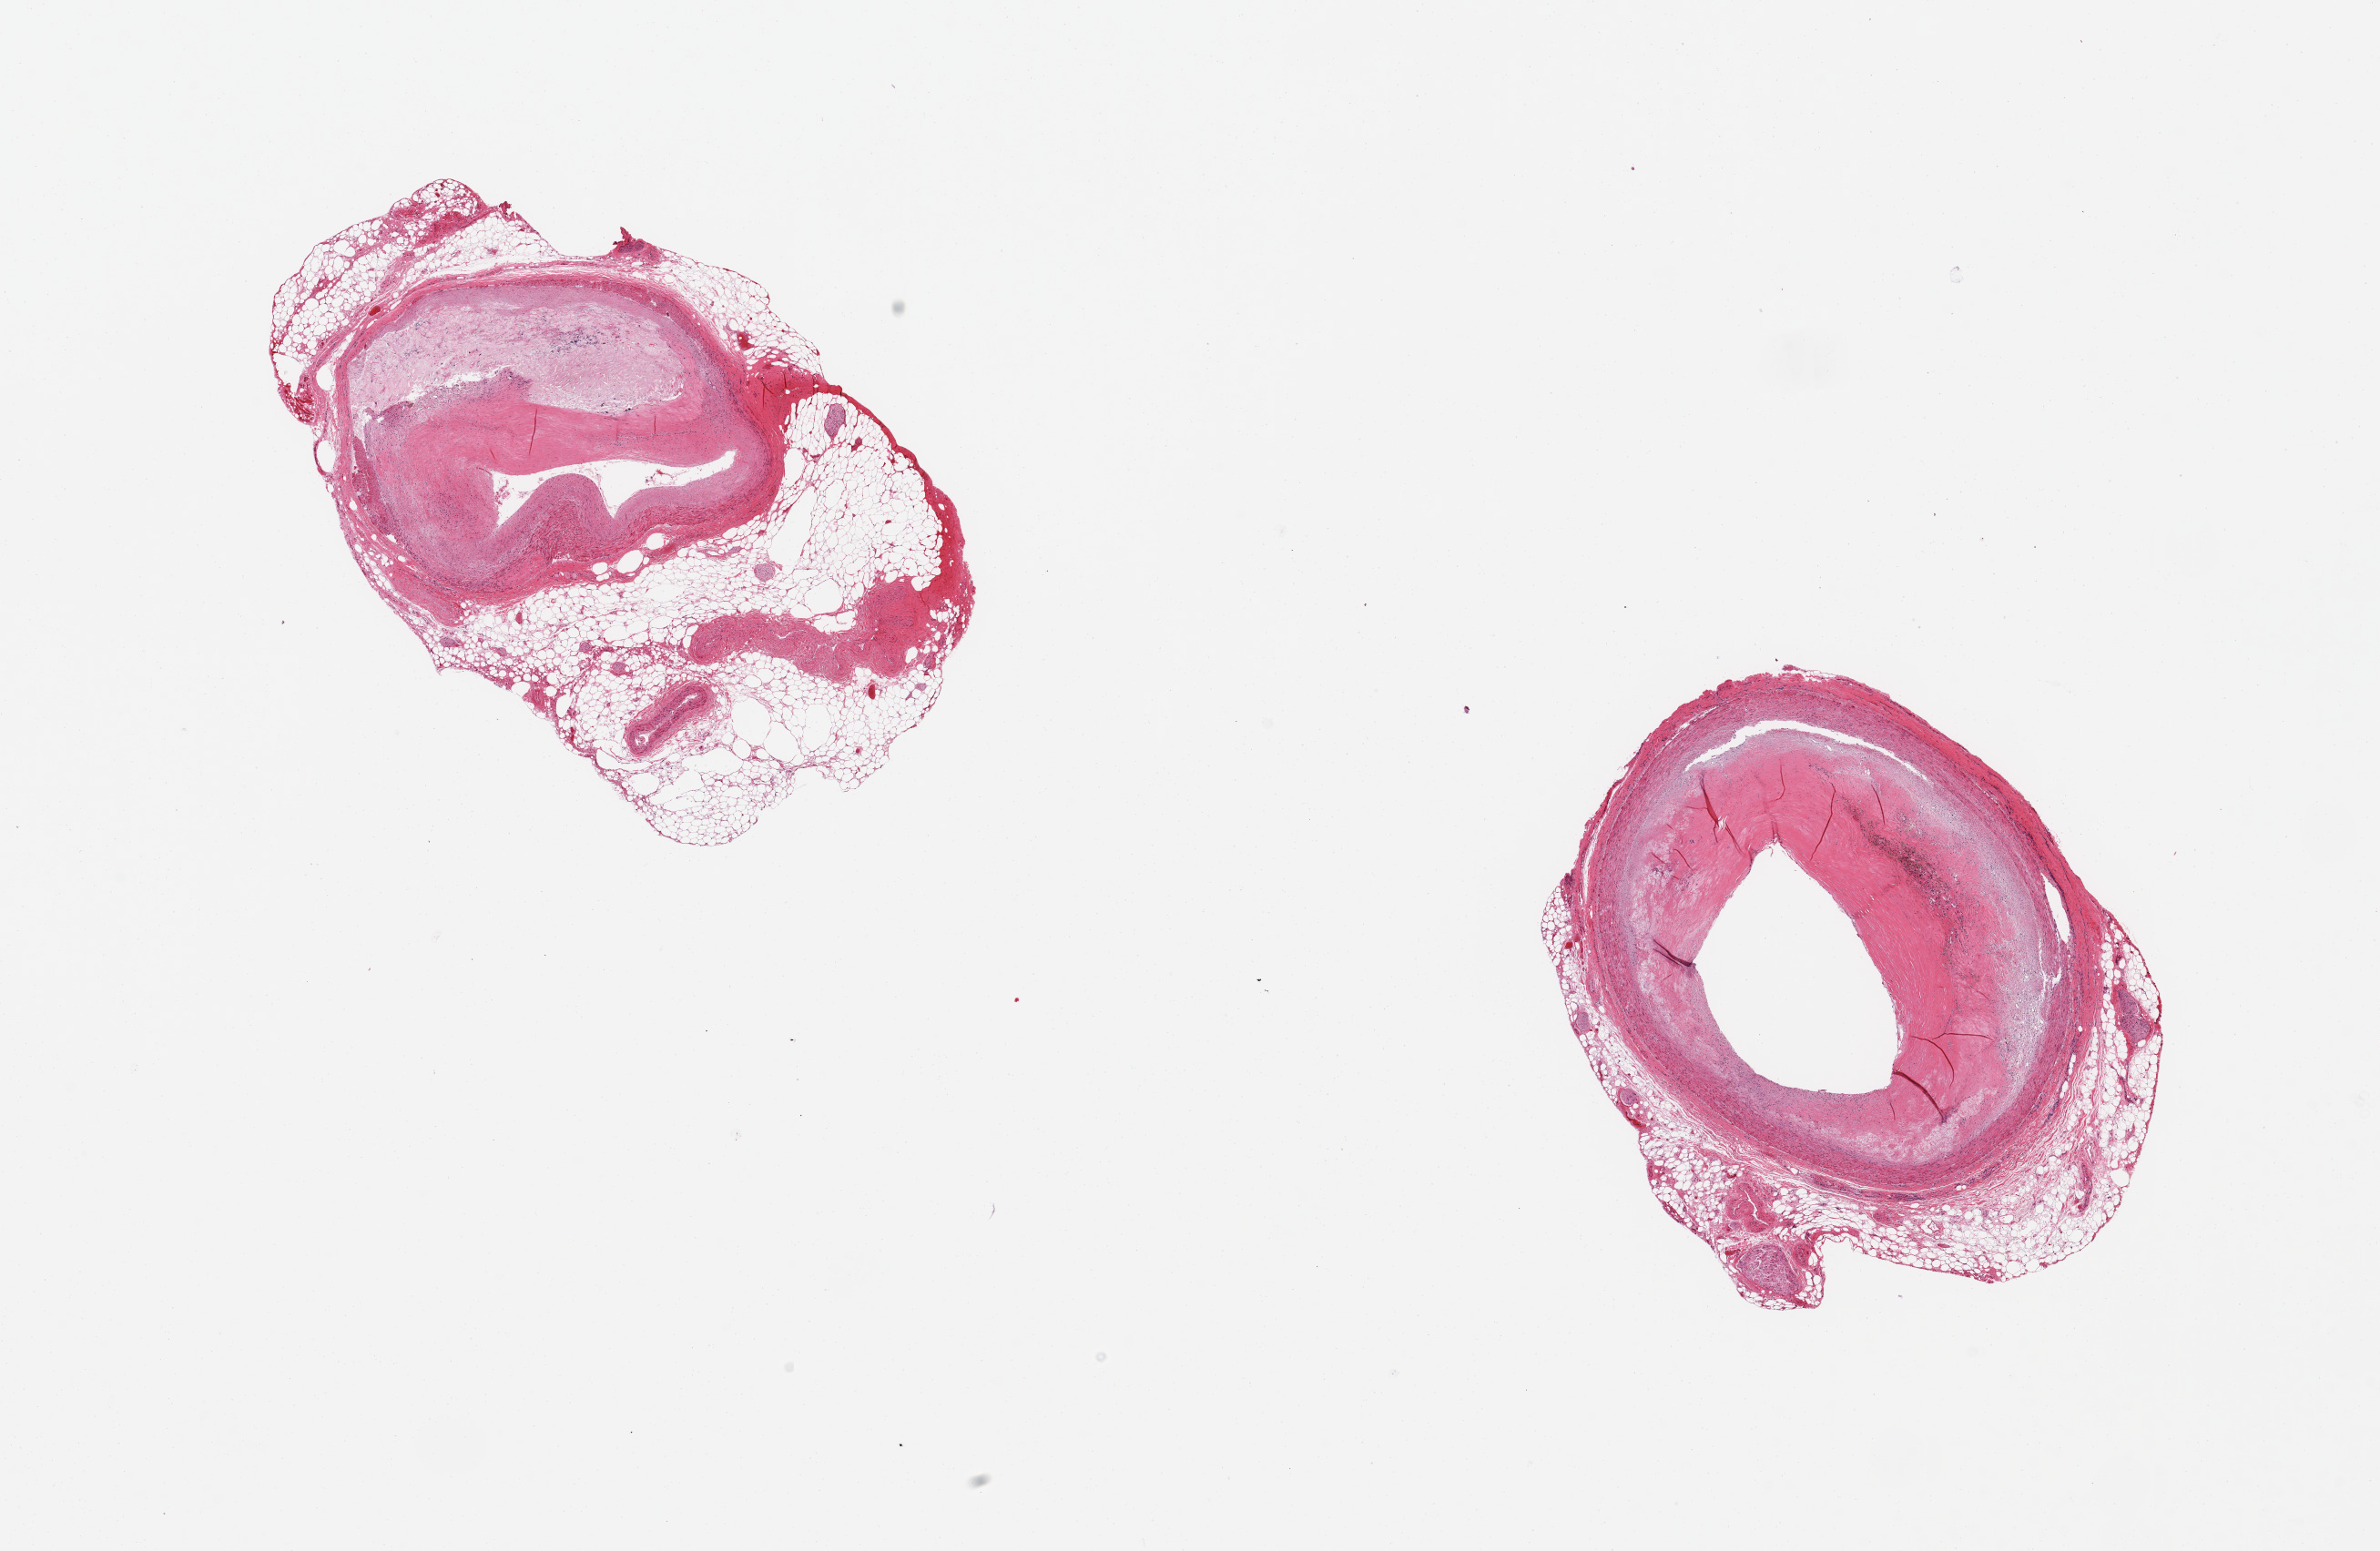
Whole-slide image, H&E stain, brightfield — whole scanned area (about 20.7 x 13.5 mm) shown as a low-resolution overview, PAXgene-fixed, paraffin-embedded tissue, section of coronary artery (target tissue), donor tissue sample. Male donor.
Review note (as recorded): 2 pieces; atheromatous plaque with hemosiderinophages (?old organized thrombus) narrowing the lumen by ~ 90% and 75%; 2.5mm and 1.2mm attached congested adventitia with fat and nerves.